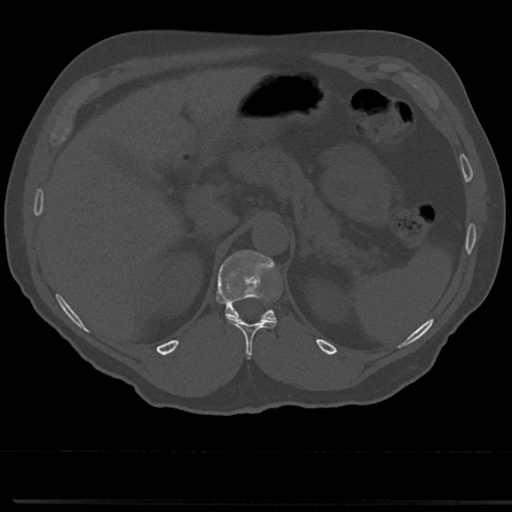
CT including the spine, one axial slice; reconstruction kernel Br40s/3; 120 kVp; bone window (W 1800 / L 400 HU); 512 × 512 image matrix, field of view 355 × 355 mm. Male patient, age 61 years. From the clinical record (not read from this slice): primary cancer: prostate.
Outlined on this slice (semi-automatic segmentation, software-assisted and operator-edited):
- T11 vertebra: bounding box <228,318,276,359> (left, top, right, bottom; pixels)
- T12 vertebra: <216,250,281,322>